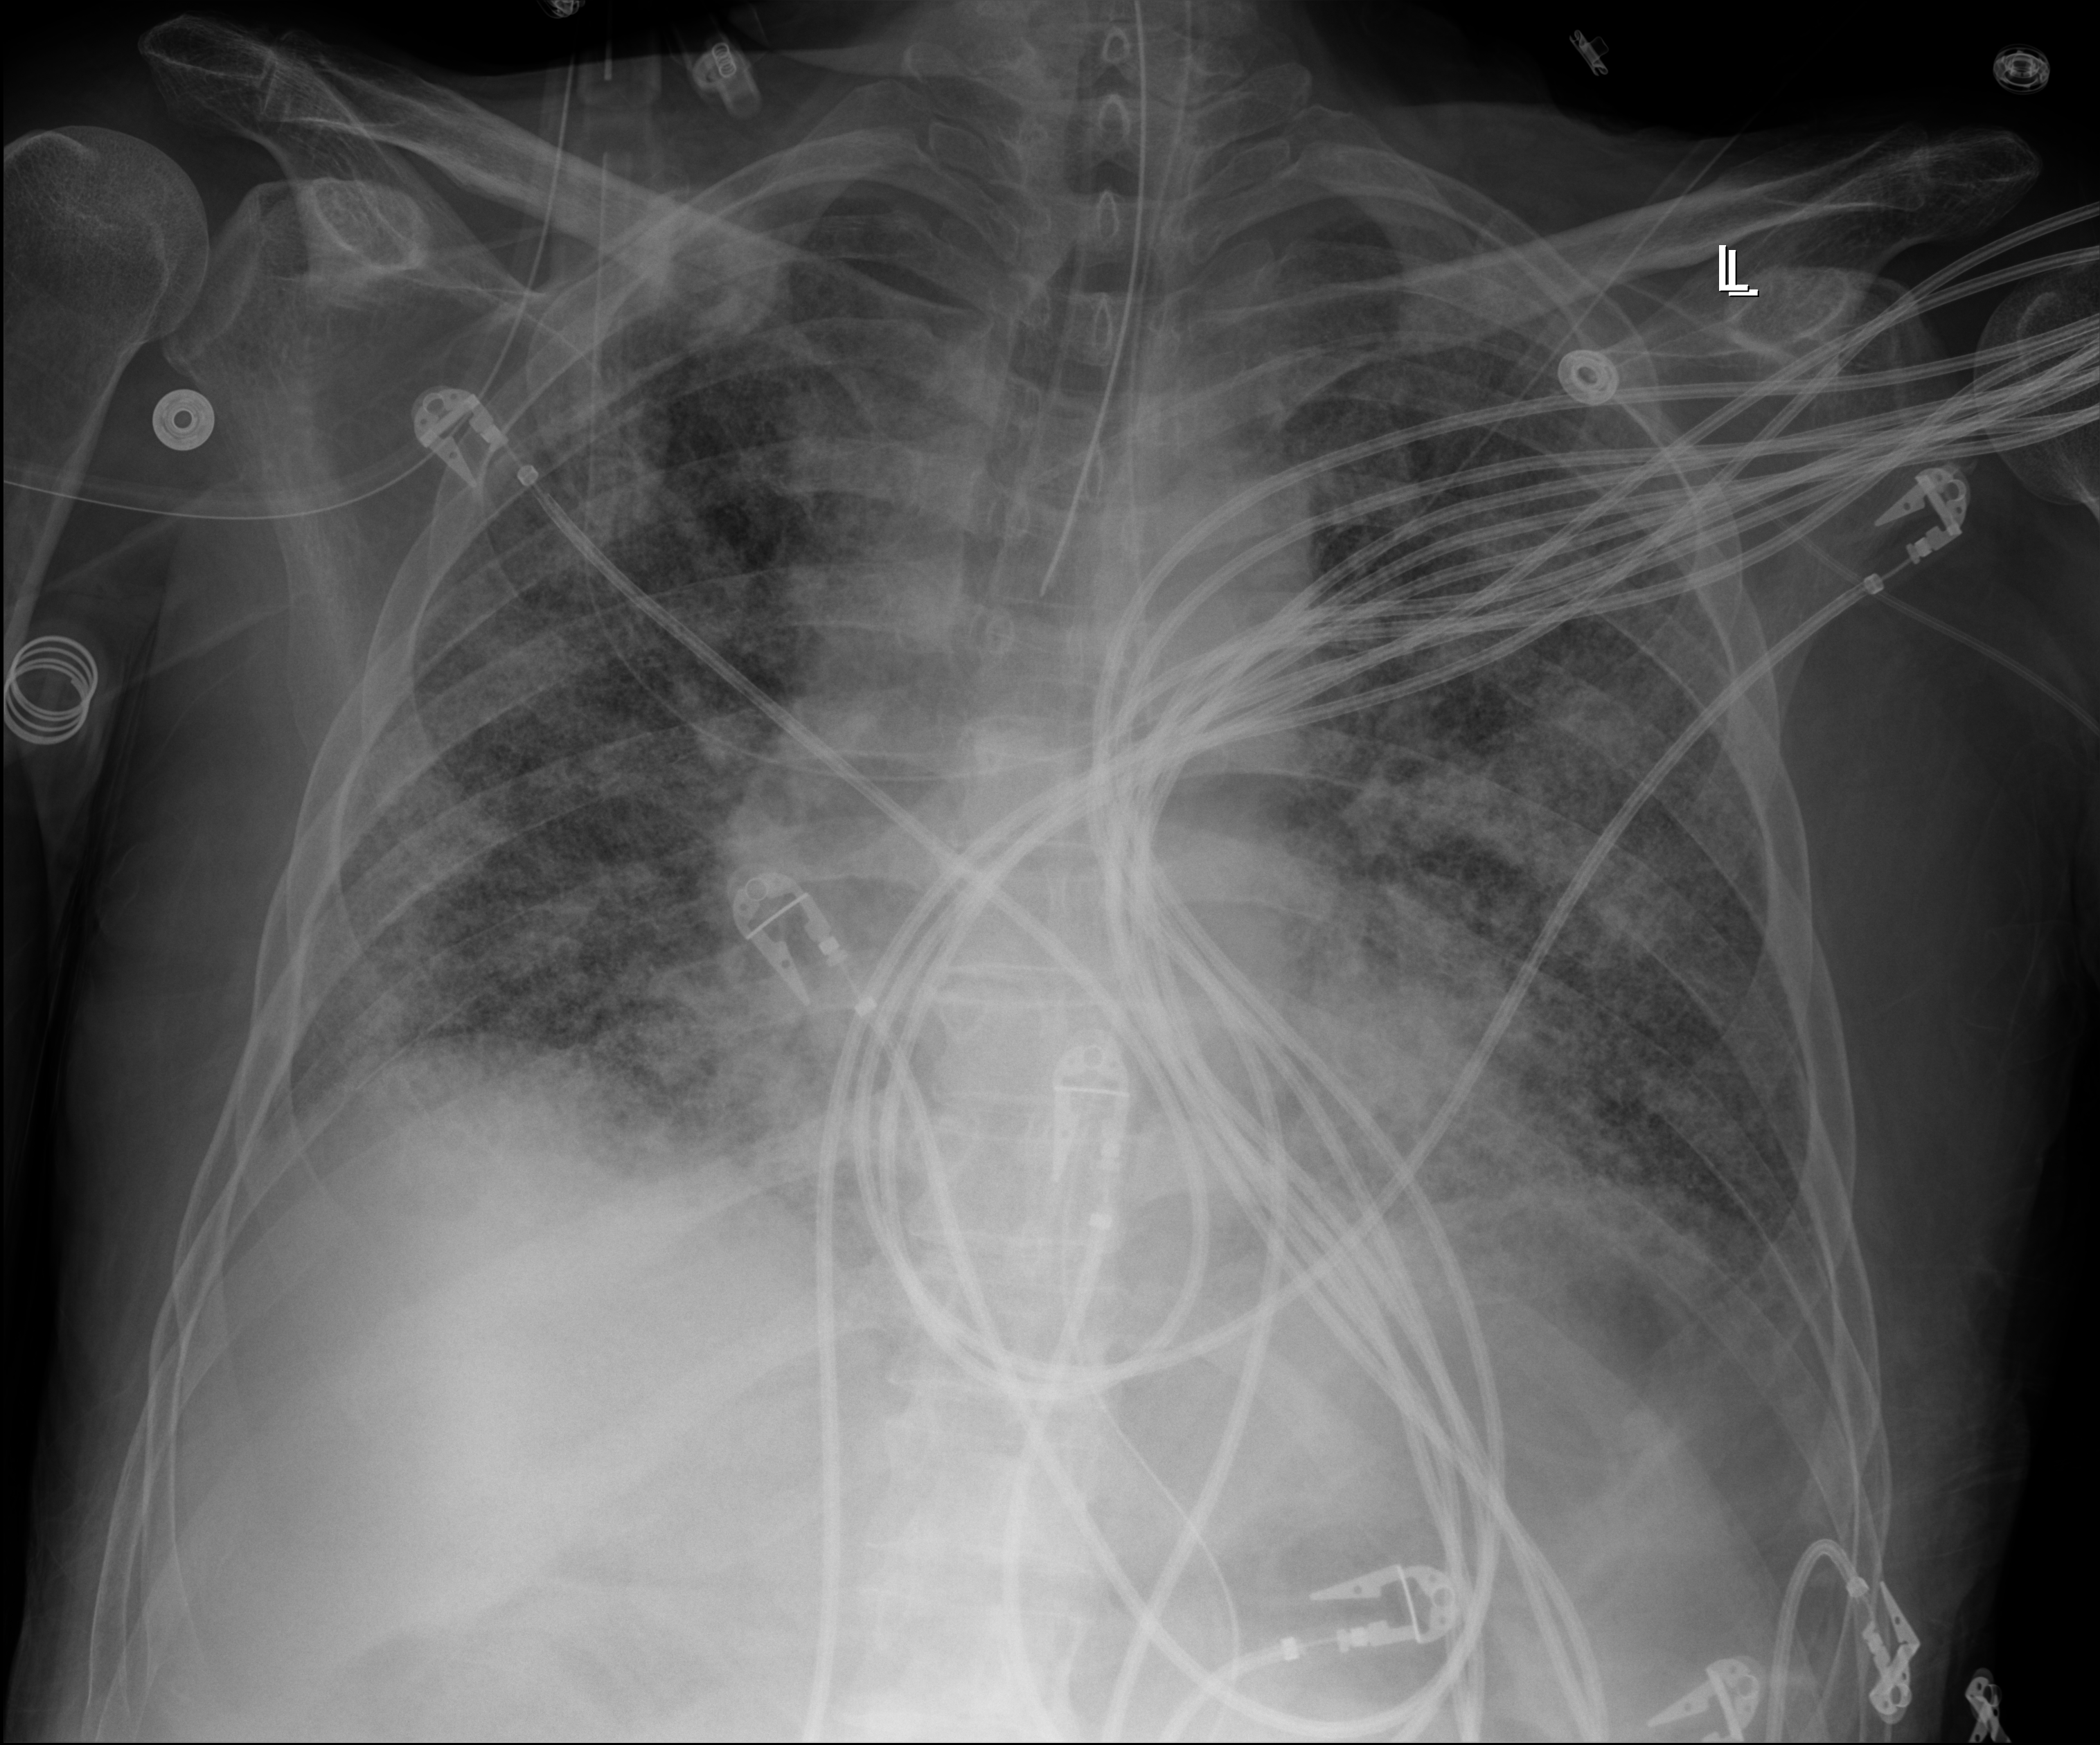
Portable chest radiograph; anteroposterior (AP) projection. Male patient hospitalised with COVID-19, age 60–74 years.
From the hospital-stay record, not from the radiograph (when in the stay this image was taken is not recorded): admitted to intensive care during this hospital stay: yes.